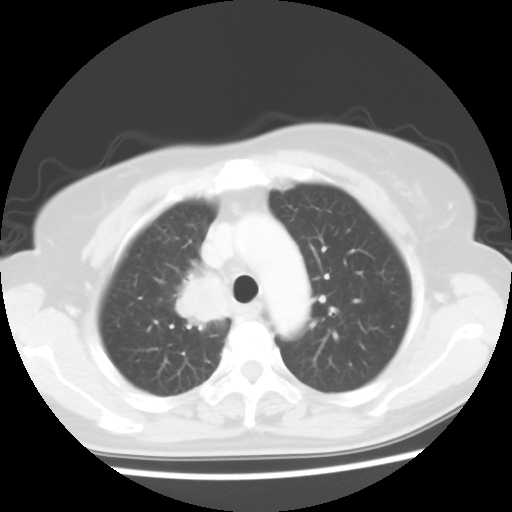
Chest CT, one axial slice; position 43 of 56 along the scan axis; reconstruction kernel STANDARD; 120 kVp; lung window (W 1500 / L -600 HU); 5 mm slice thickness; 512 × 512 image matrix. Patient: female, 62 years. From the clinical record (not read from this slice): clinical TNM (as recorded): T2 N1 M1a.
Structures marked on this image (bounding box drawn by a radiologist):
- lung tumour (recorded histology: adenocarcinoma): bounding box (x1, y1, x2, y2) in pixels: (161, 253, 242, 340)